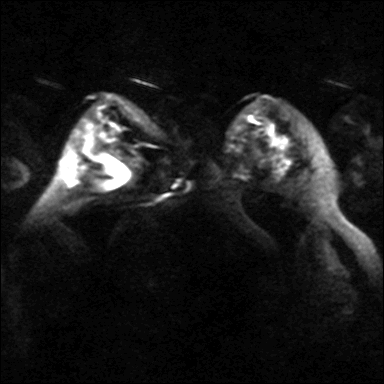
Breast MRI, one axial slice. Slice 24 of 40 in the series (ordered by position). Diffusion-weighted series; image 2 of 4 stored at this slice position (different b-values; order by instance number). 3 T. 4 mm slice thickness. 384 × 384 image matrix, field of view 320 × 320 mm. Female patient.
Outlined on this slice (outlined manually by an expert reader):
- tumour on diffusion-weighted imaging: bounding box [x1, y1, x2, y2] px = [266, 121, 271, 131]